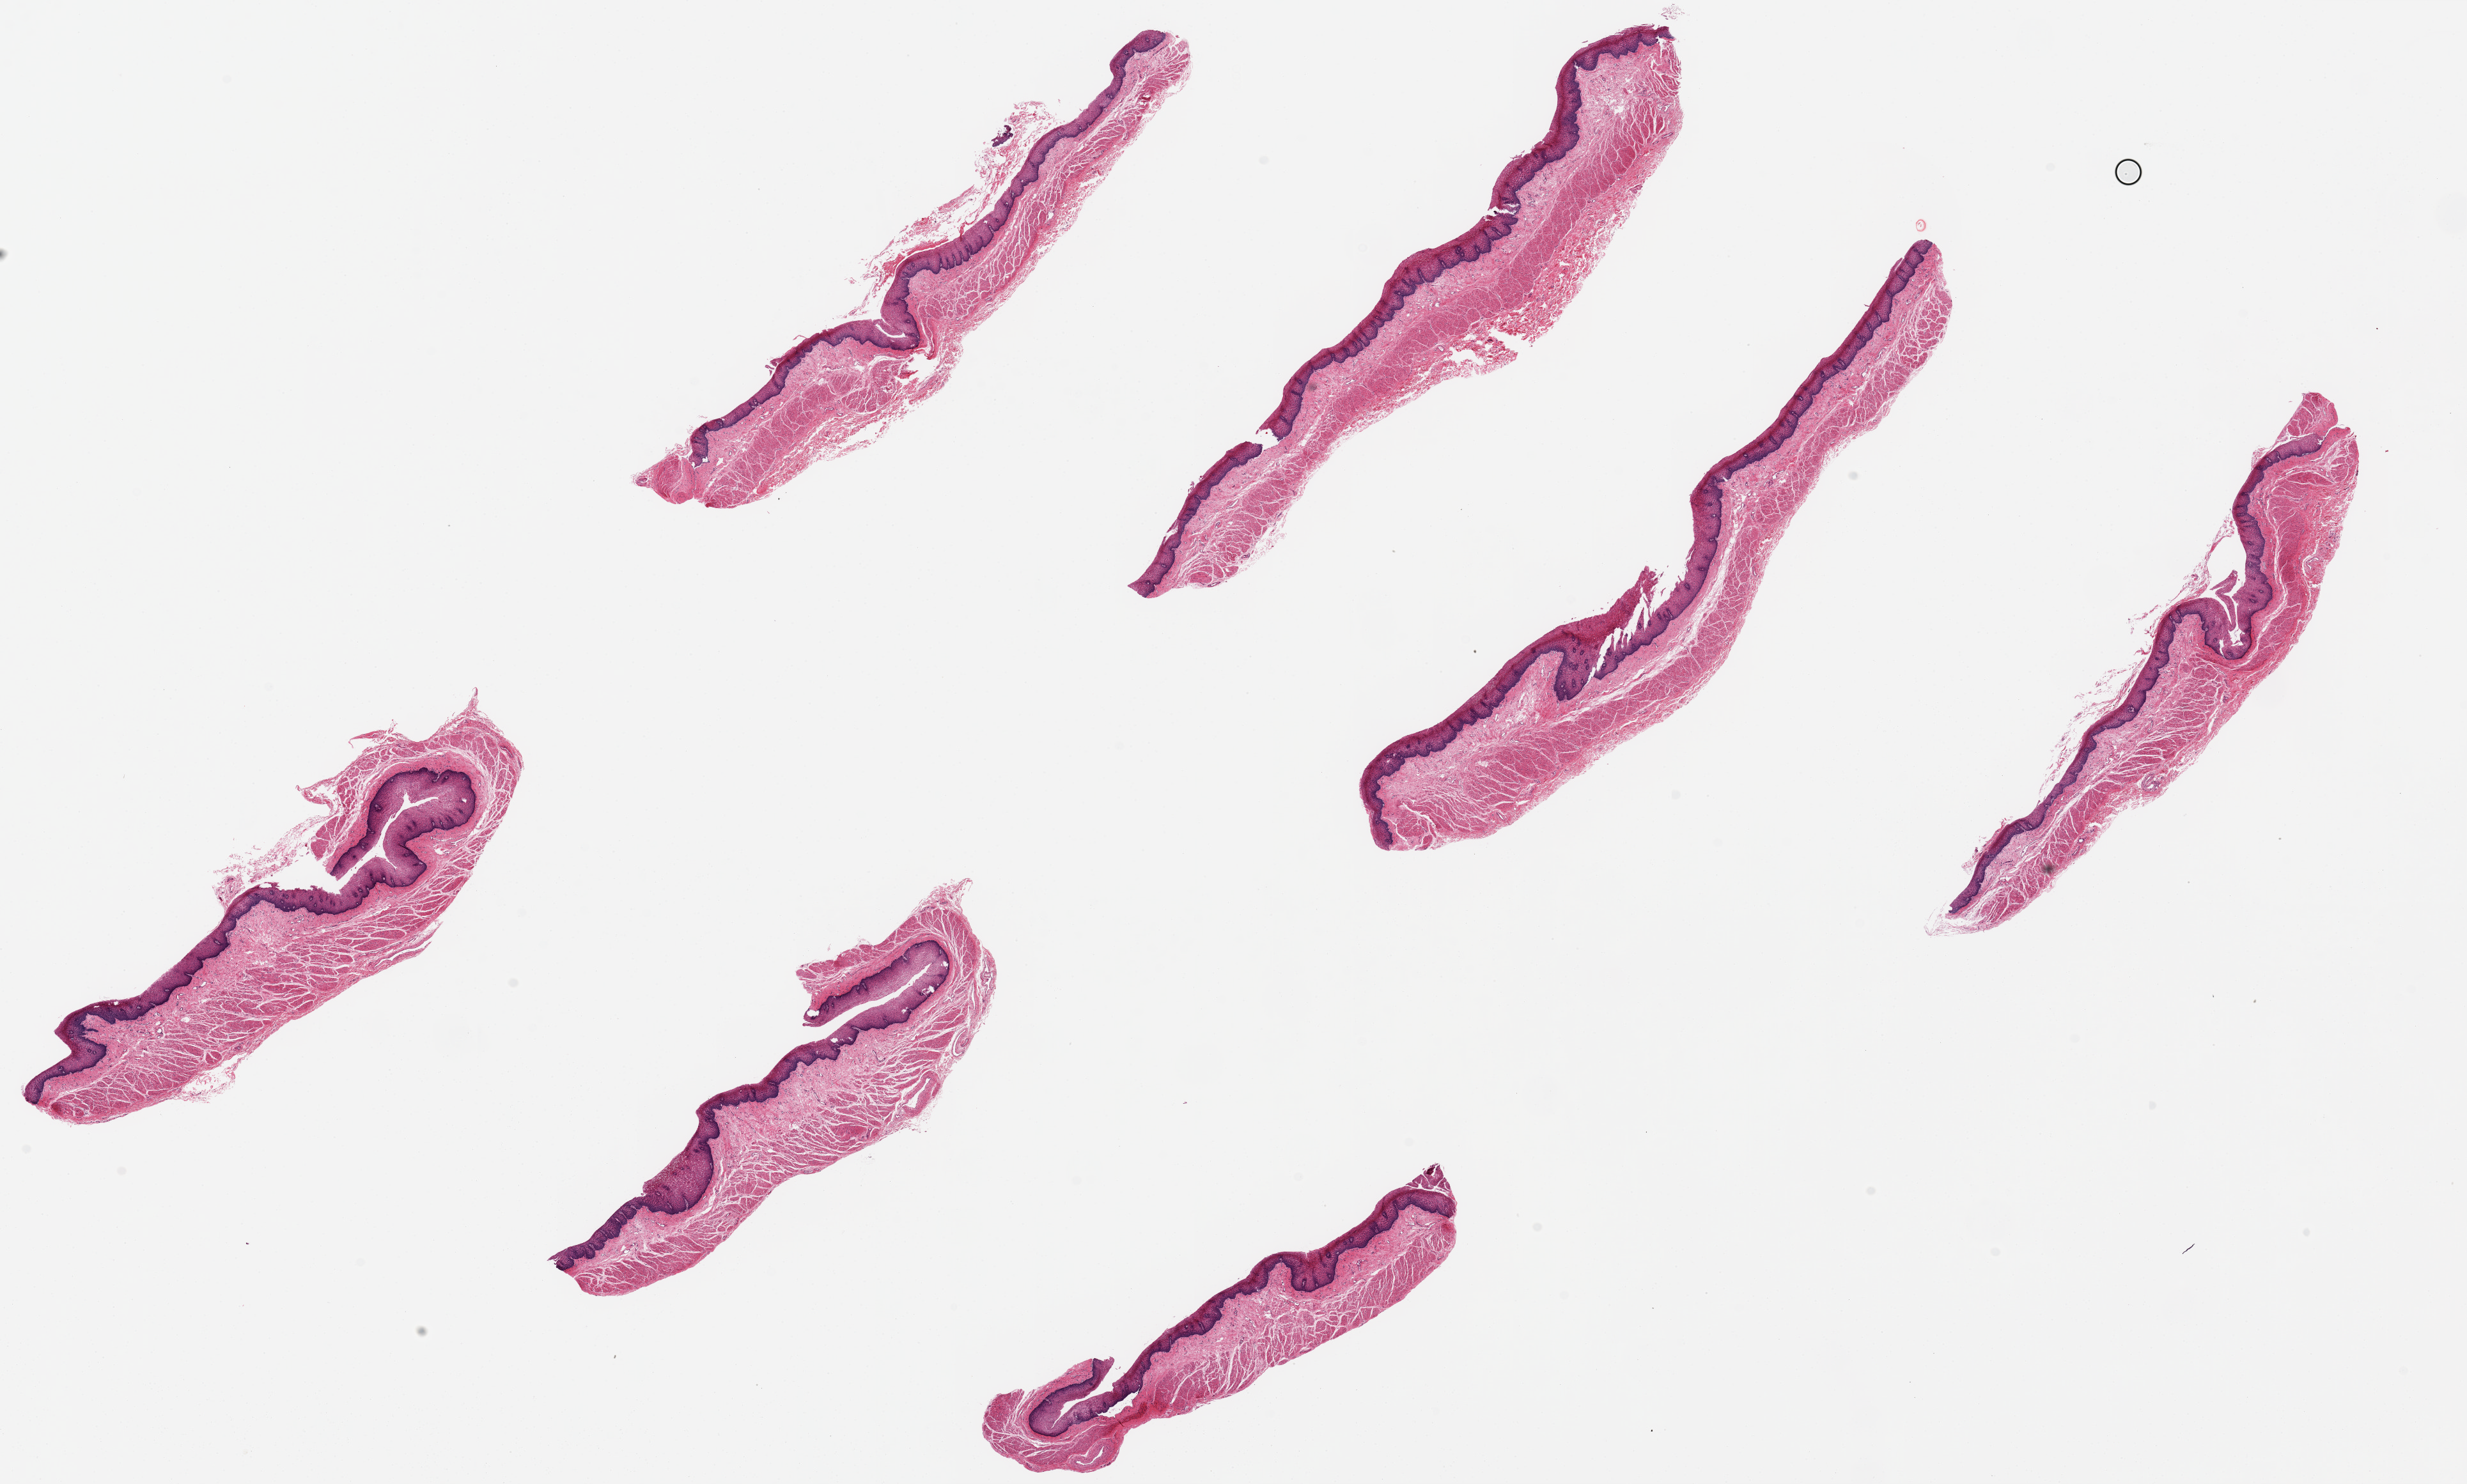
Hematoxylin and eosin (H&E) whole-slide image, brightfield — whole scanned area (about 30.5 x 18.4 mm, from a 20x scan) shown as a low-resolution overview; PAXgene-fixed, paraffin-embedded tissue; section of esophageal mucous membrane (target tissue); donor tissue sample. Female donor.
Review note (as recorded): 6 pieces, ~9x1.5mm. Squamous mucosa is ~15-20% of thickness.